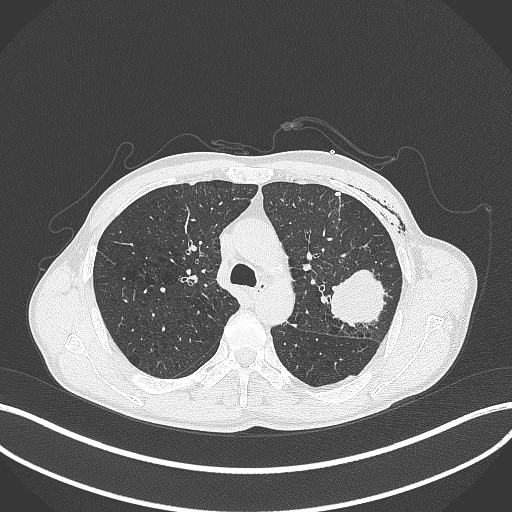
Chest CT, one axial slice. Slice 279 of 457 in the series (ordered by position). 120 kVp. Lung window (W 1500 / L -600 HU). 1 mm slice thickness. 512 × 512 image matrix, field of view 400 × 400 mm. Patient: male, 58 years. Case-level facts recorded for this patient, not image findings: clinical TNM (as recorded): T3 N0 M0.
Outlined on this slice (rectangle marked by the reading radiologist):
- lung tumour (recorded histology: adenocarcinoma): bounding box (x1, y1, x2, y2) in pixels: (329, 264, 389, 325)